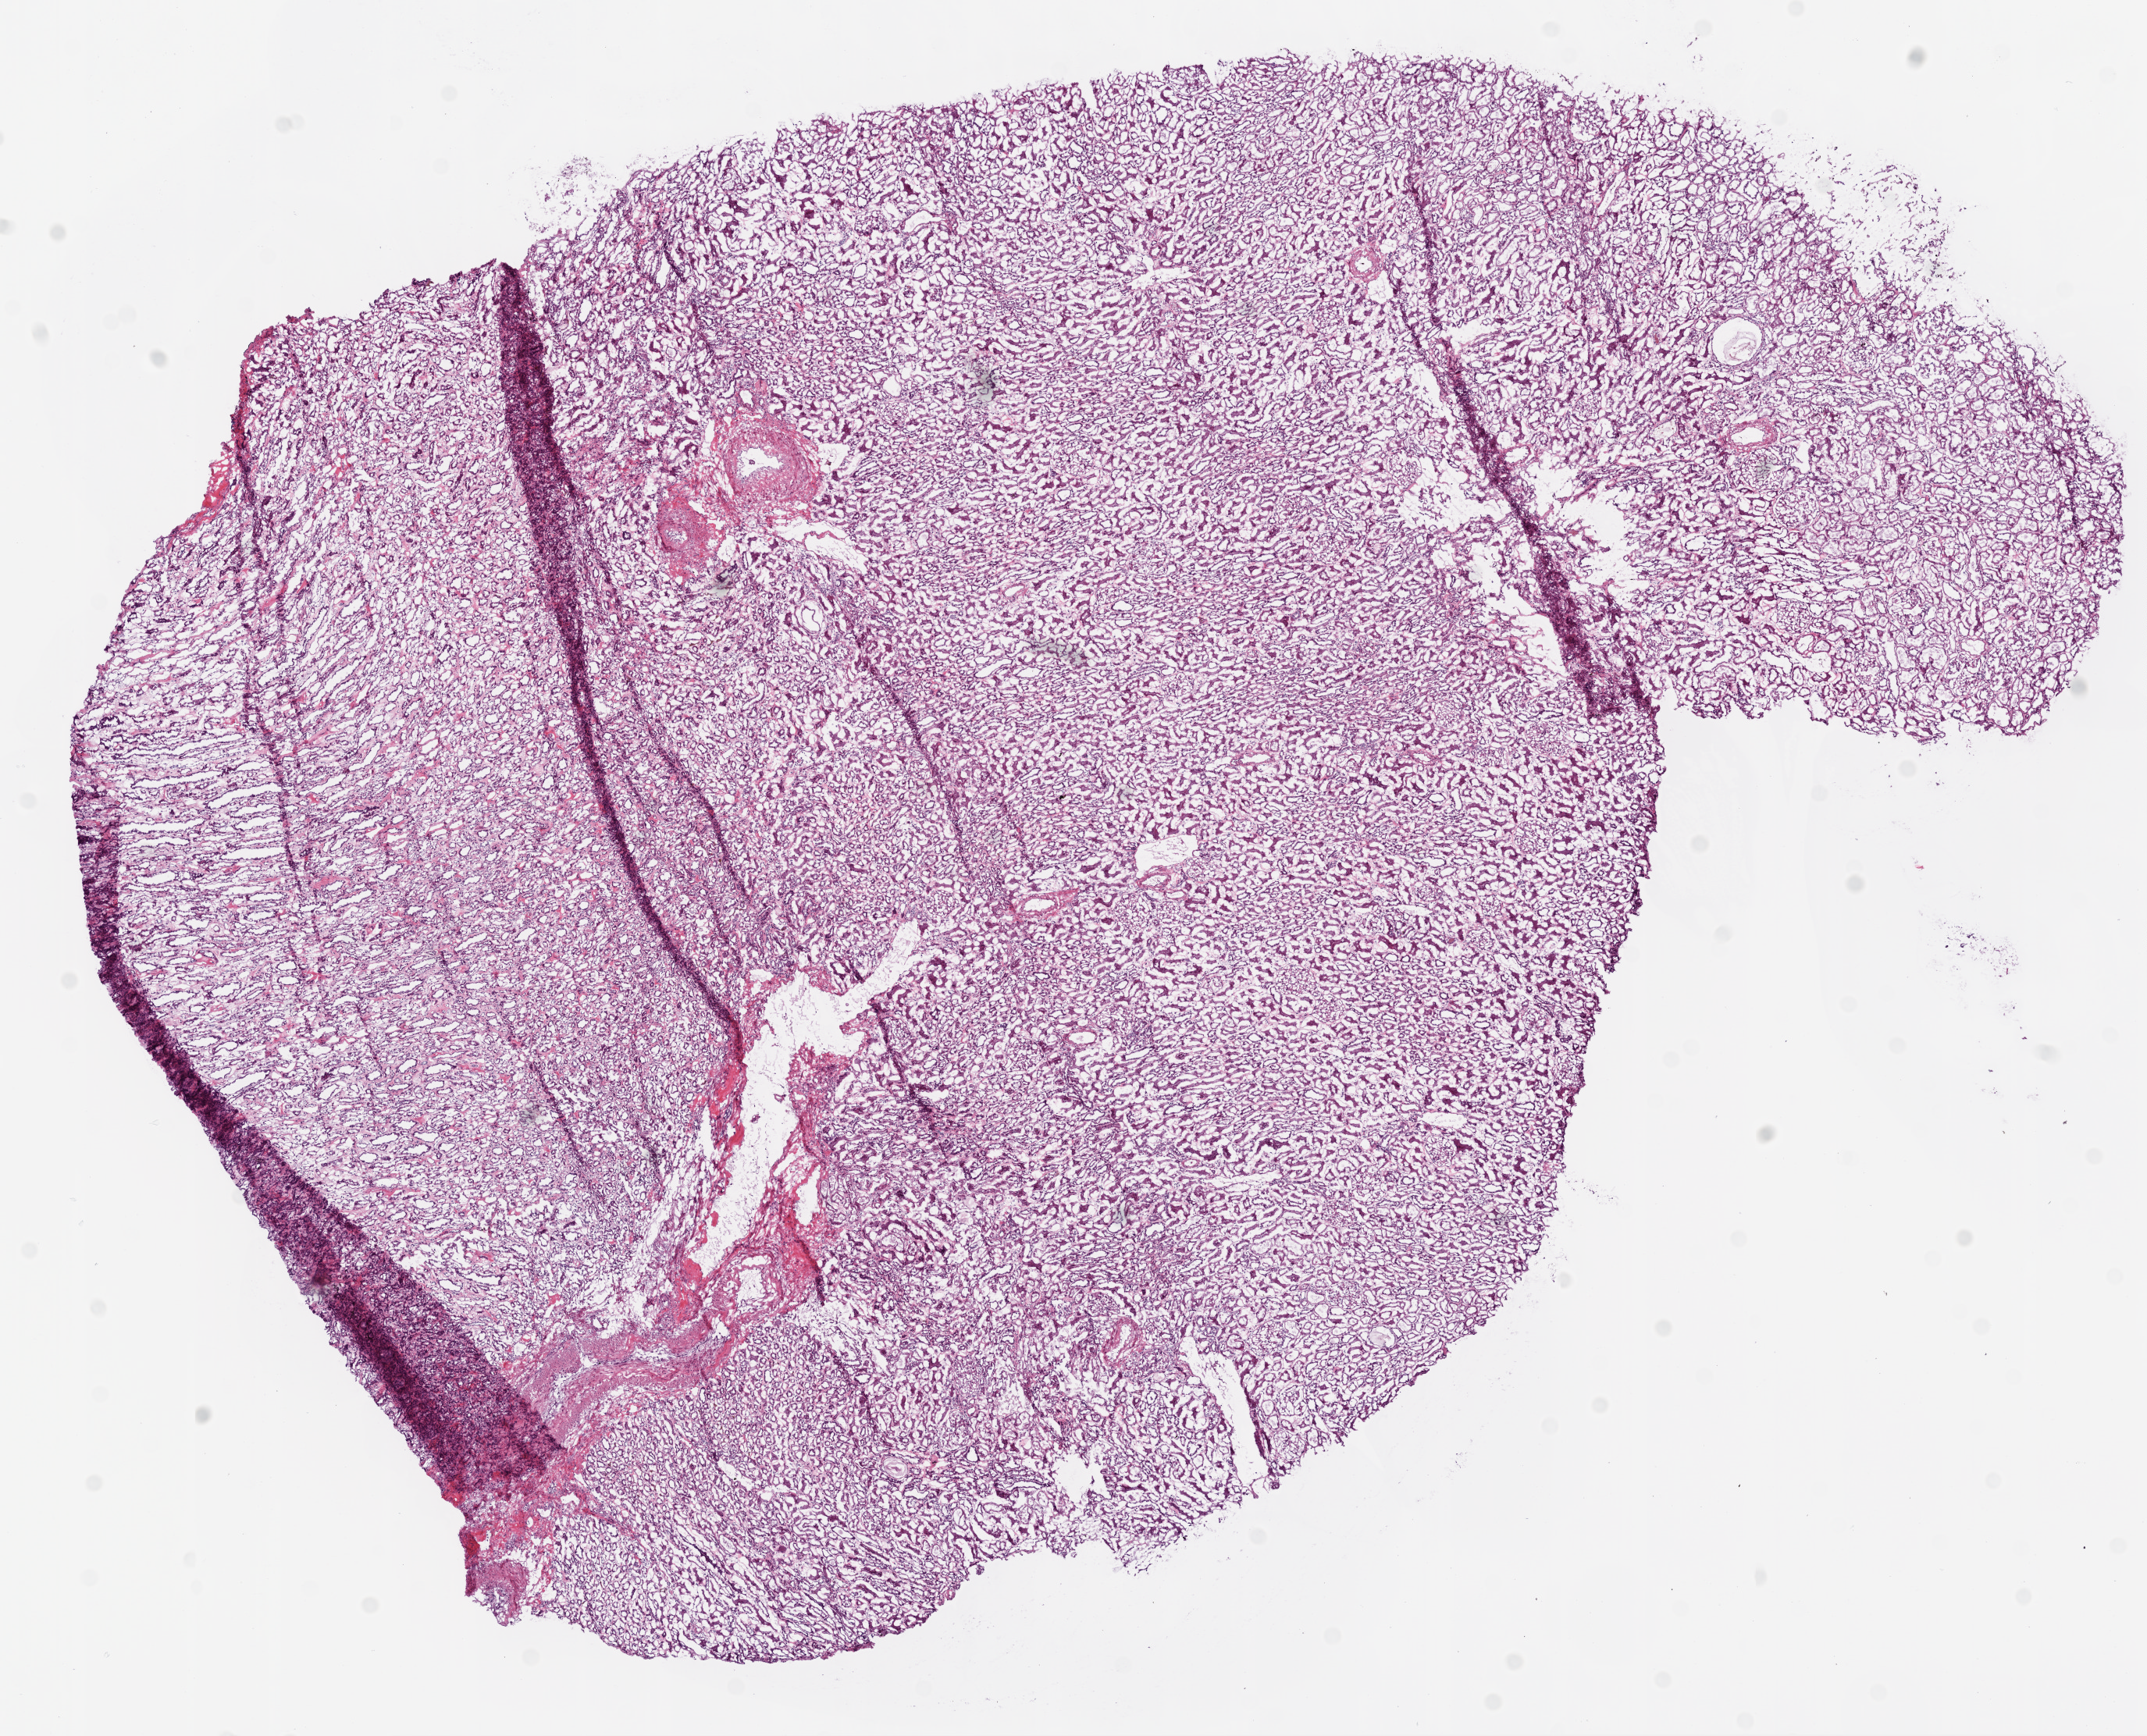
Hematoxylin and eosin (H&E) stained whole-slide image, shown as a low-resolution overview of the whole scanned area (about 11.0 x 8.9 mm). Frozen section from the top of the tissue portion. Kidney, solid tissue normal (non-tumour tissue) sample. Male patient; age at initial diagnosis 46 years.
This section: solid tissue normal (non-tumour) sample from the same patient. Patient diagnosis: Clear cell adenocarcinoma, NOS.